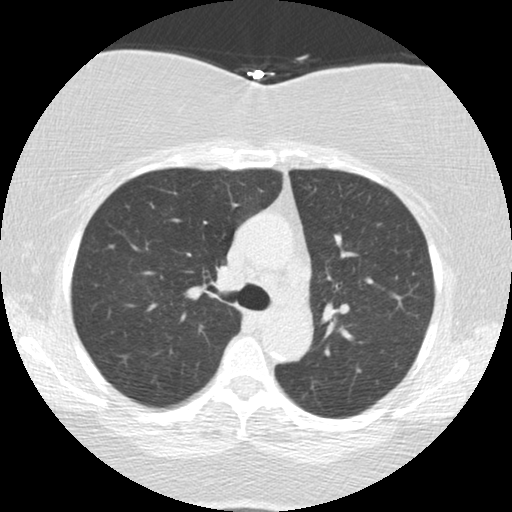
Low-dose screening chest CT, one axial slice. Slice 93 of 136 in the series (ordered by position). Reconstruction kernel STANDARD. 120 kVp. Lung window (W 1500 / L -600 HU). 2.5 mm slice thickness. 512 × 512 image matrix.
Annotated regions visible in this slice (outlined manually by an expert reader):
- lesion 1 (tumor): bounding box [x1, y1, x2, y2] px = [217, 265, 241, 288]